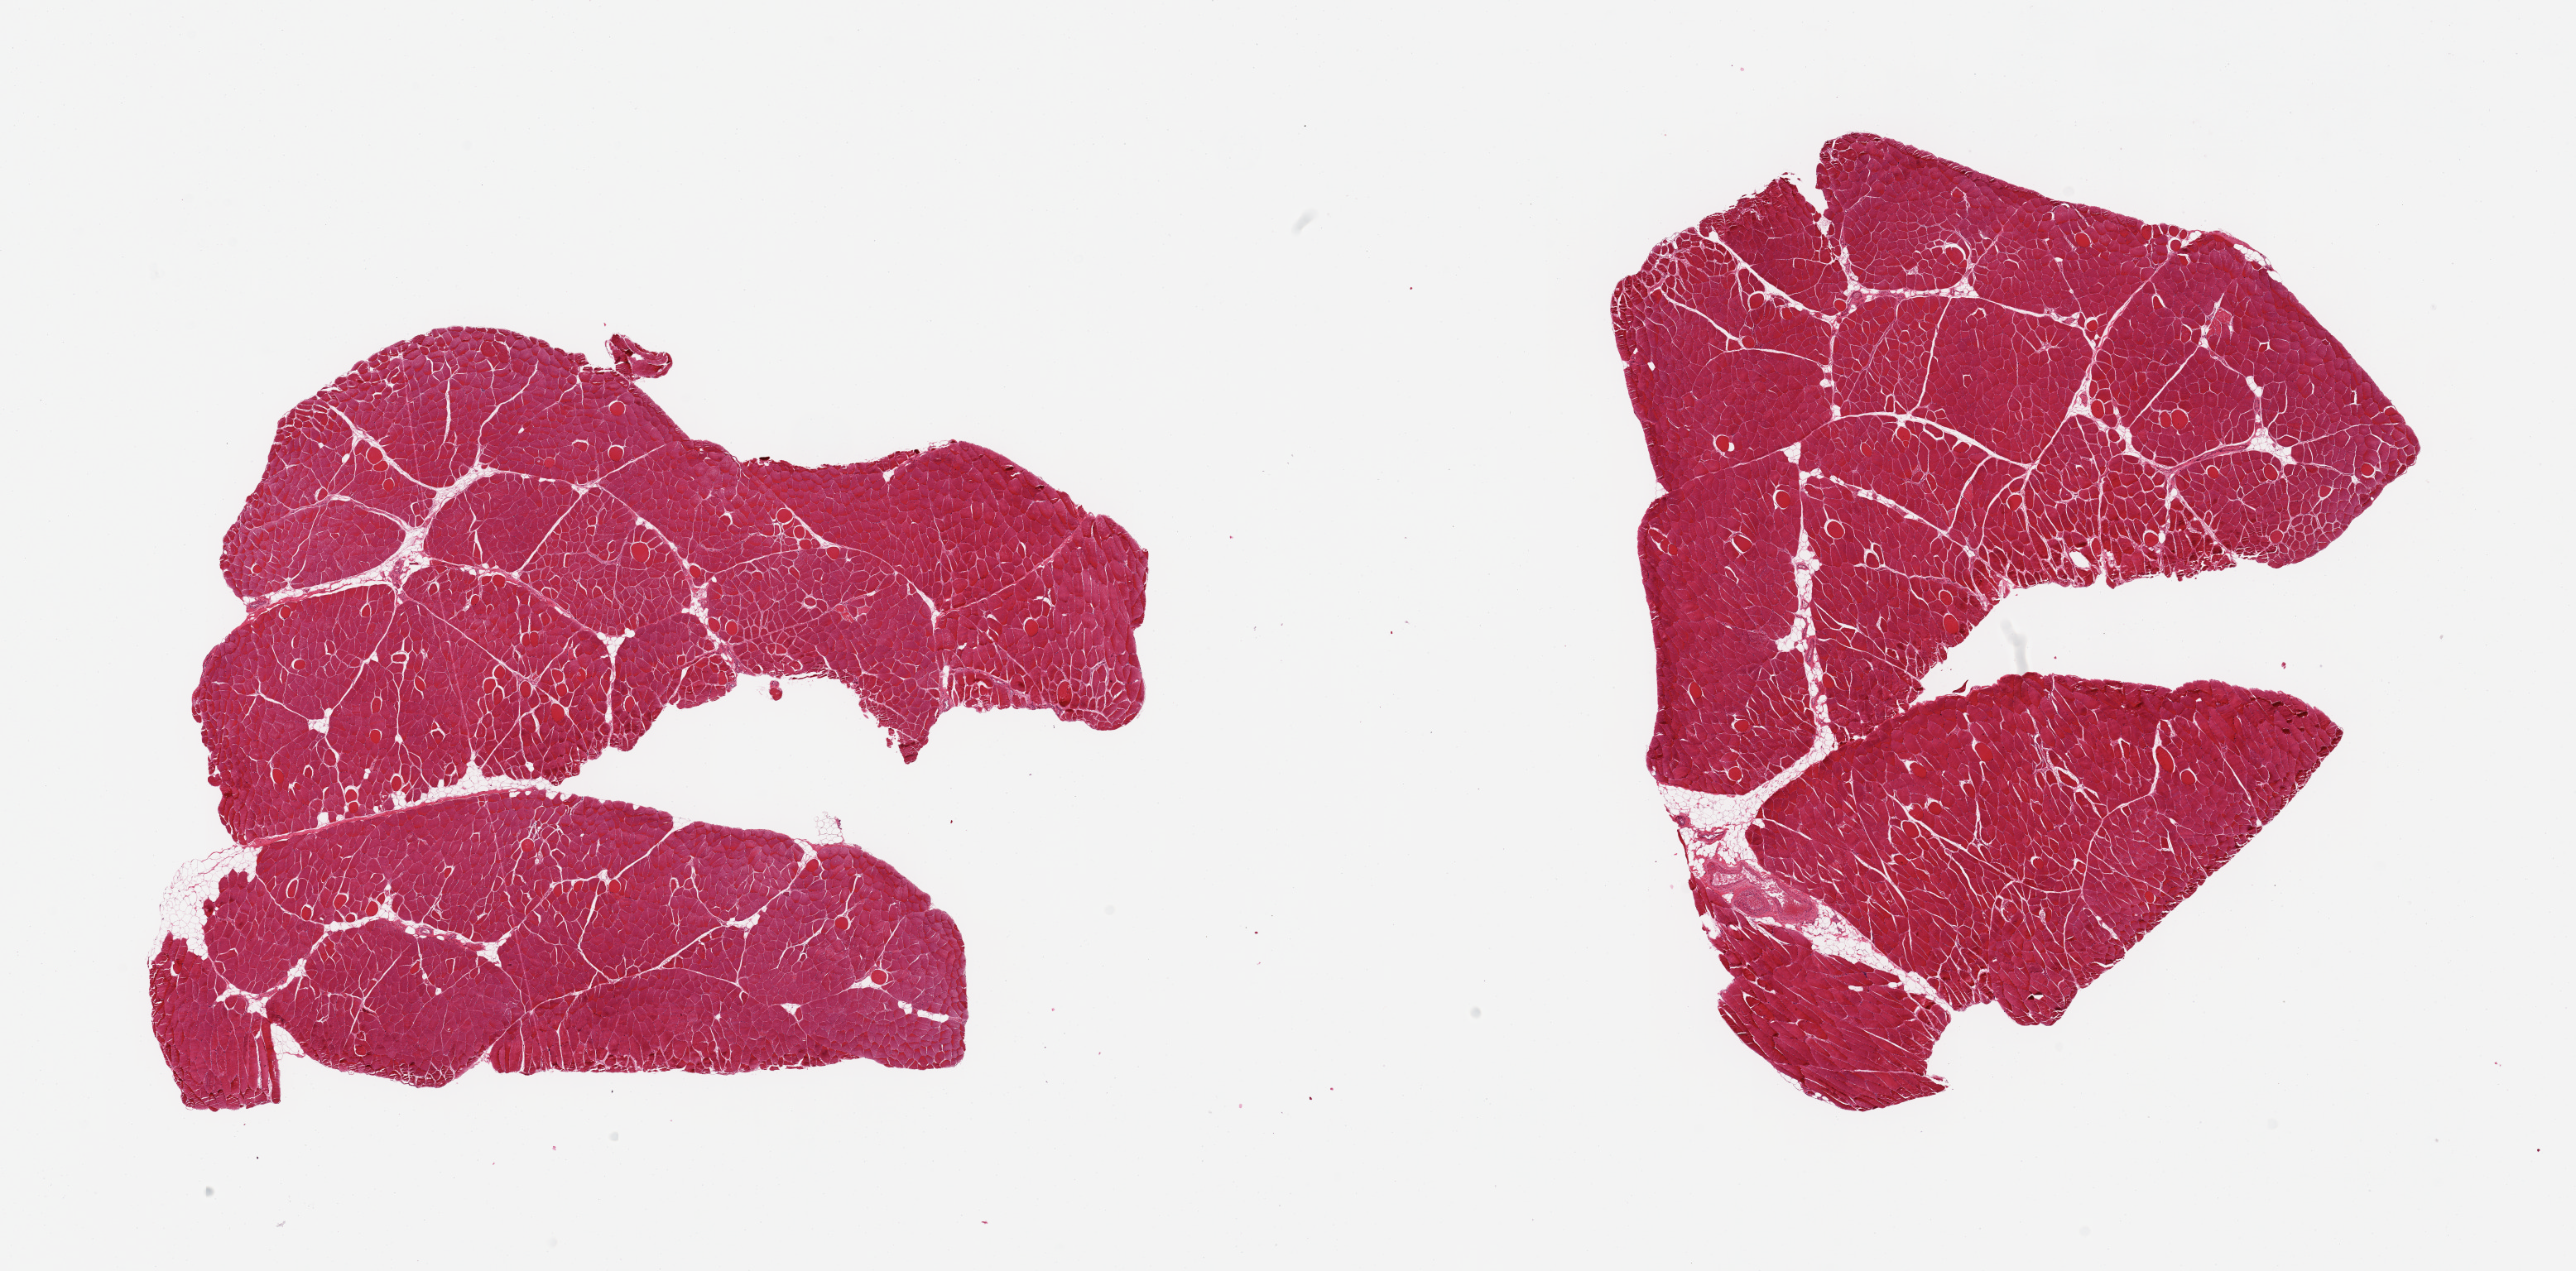
Whole-slide image, hematoxylin and eosin (H&E) stain — low-resolution overview of the scanned area, about 24.6 x 12.1 mm, PAXgene-fixed, paraffin-embedded tissue, sampled site (target tissue): skeletal muscle, donor tissue sample. Donor: male.
Reviewer comment on this tissue sample: 2 pieces; minimal internal fat.